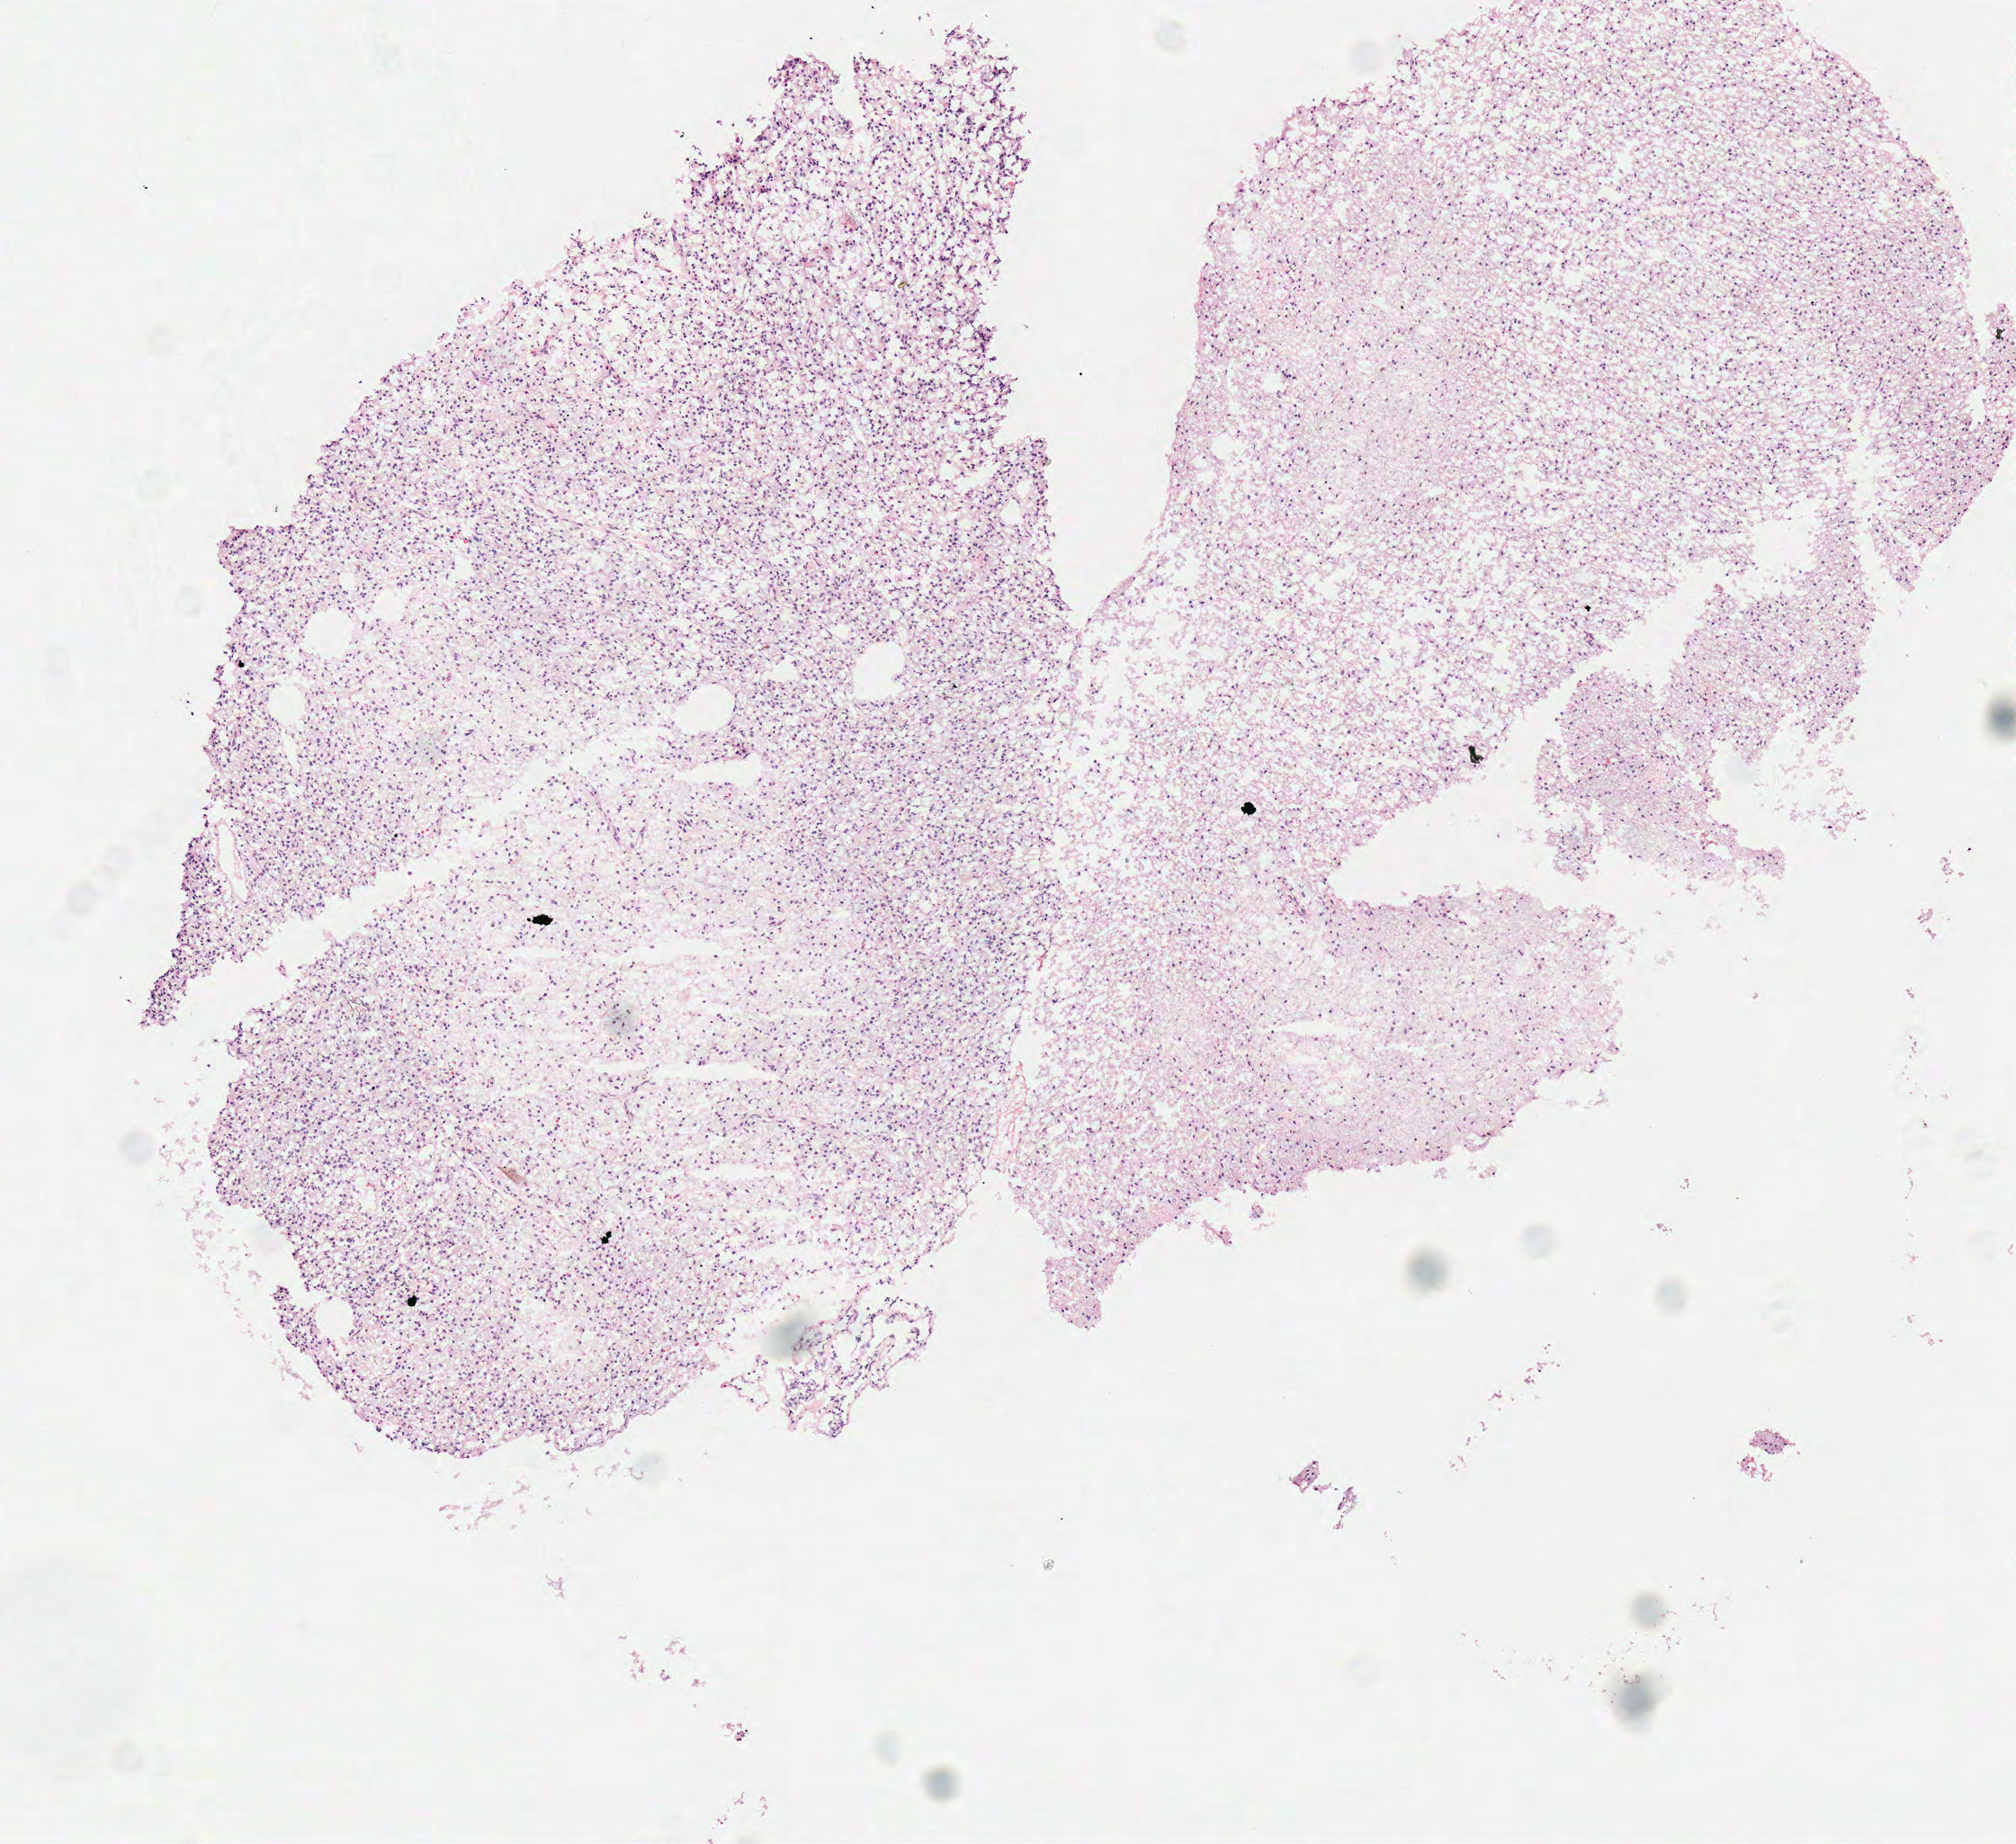
H&E-stained whole-slide image — a low-resolution overview of the entire scanned area, about 4.4 x 4.0 mm (from a 40x scan), frozen section from the top of the tissue portion, sample: primary tumour, brain. Male patient; age at initial diagnosis 63 years. Histologic grade: G3 (poorly differentiated). Slide review estimates, as recorded: tumour cells 100%, tumour nuclei 75%, normal cells 0%, stromal cells 0%, necrosis 0%.
* laterality: right
* pathologic diagnosis: Oligodendroglioma, anaplastic (cerebrum)